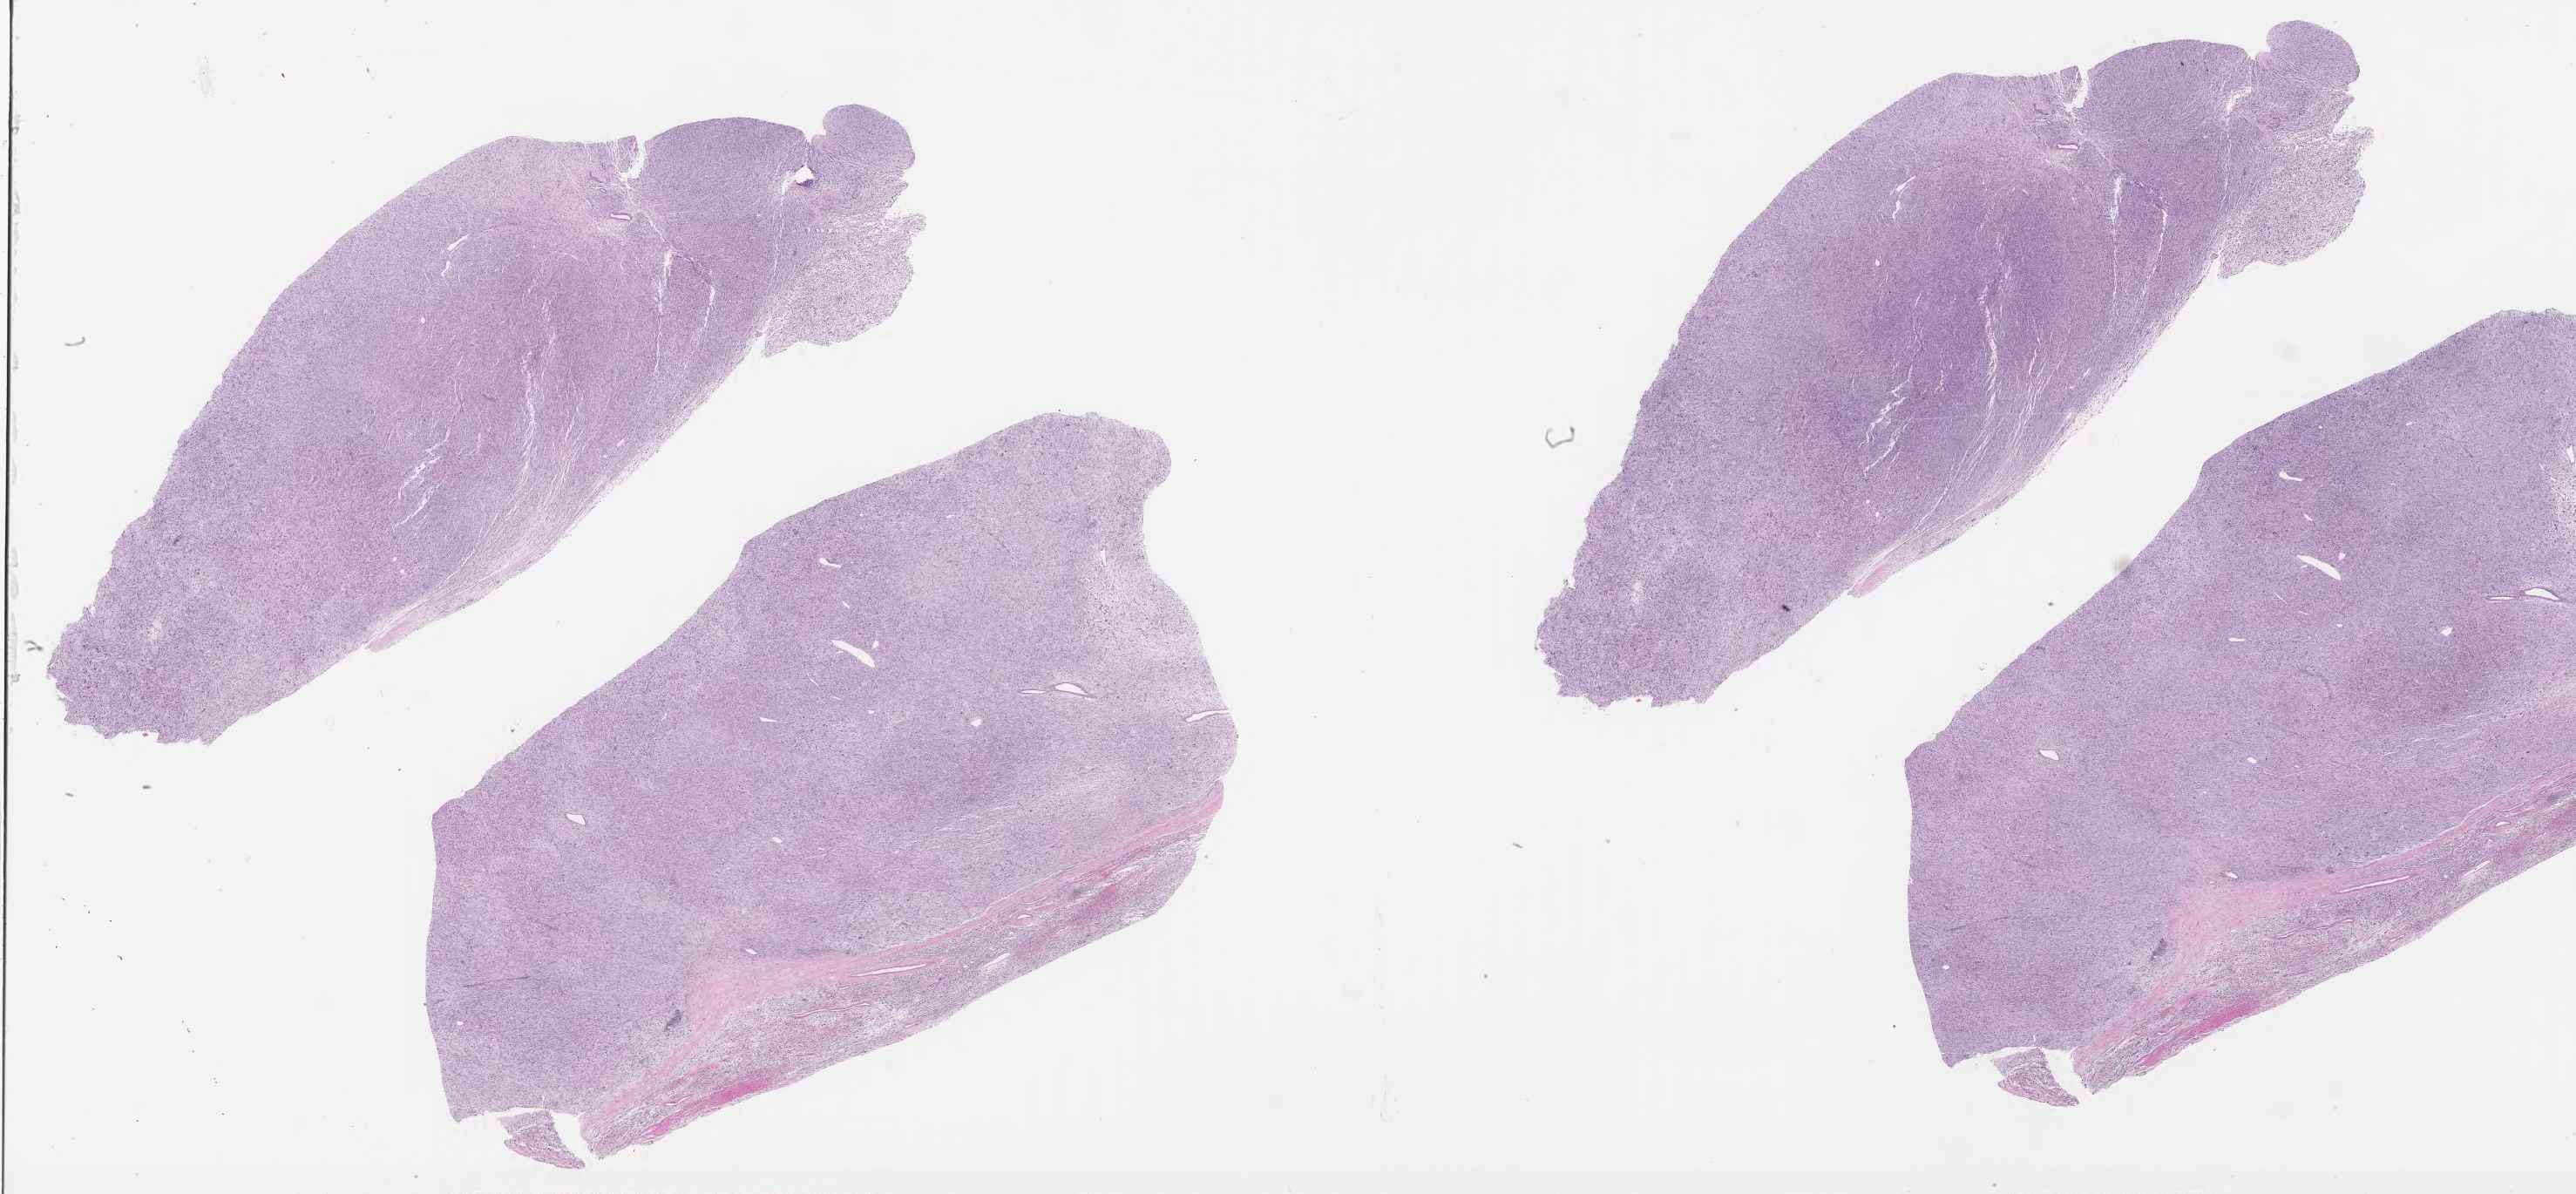
H&E-stained whole-slide image — a low-resolution overview of the entire scanned area, about 47.5 x 22.0 mm (acquisition: 40x scan), formalin-fixed paraffin-embedded (FFPE) diagnostic section, sample: primary tumour, retroperitoneum and peritoneum. Patient: female, age at initial diagnosis 79 years.
• diagnosis: Fibromyxosarcoma (retroperitoneum)